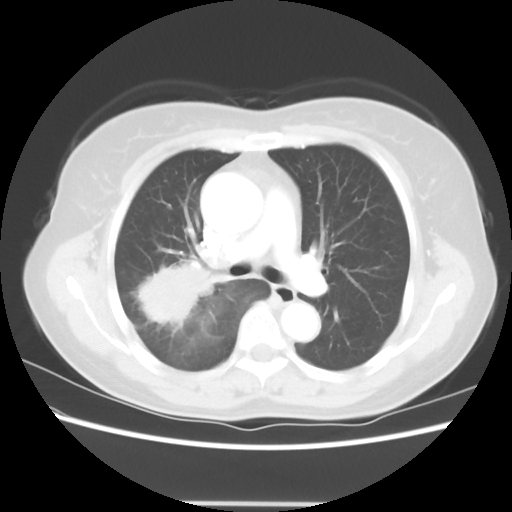
Chest CT, one axial slice. 120 kVp. Lung window (W 1500 / L -600 HU). 5 mm slice thickness. 512 × 512 image matrix, field of view 360 × 360 mm. Patient: female, 55 years. Case-level facts recorded for this patient, not image findings: clinical TNM (as recorded): T2 N1 M0; histopathological grade: G2-3.
Annotated regions visible in this slice (rectangle marked by the reading radiologist):
- lung tumour (recorded histology: adenocarcinoma): bounding box (x1, y1, x2, y2) in pixels: (128, 259, 219, 330)